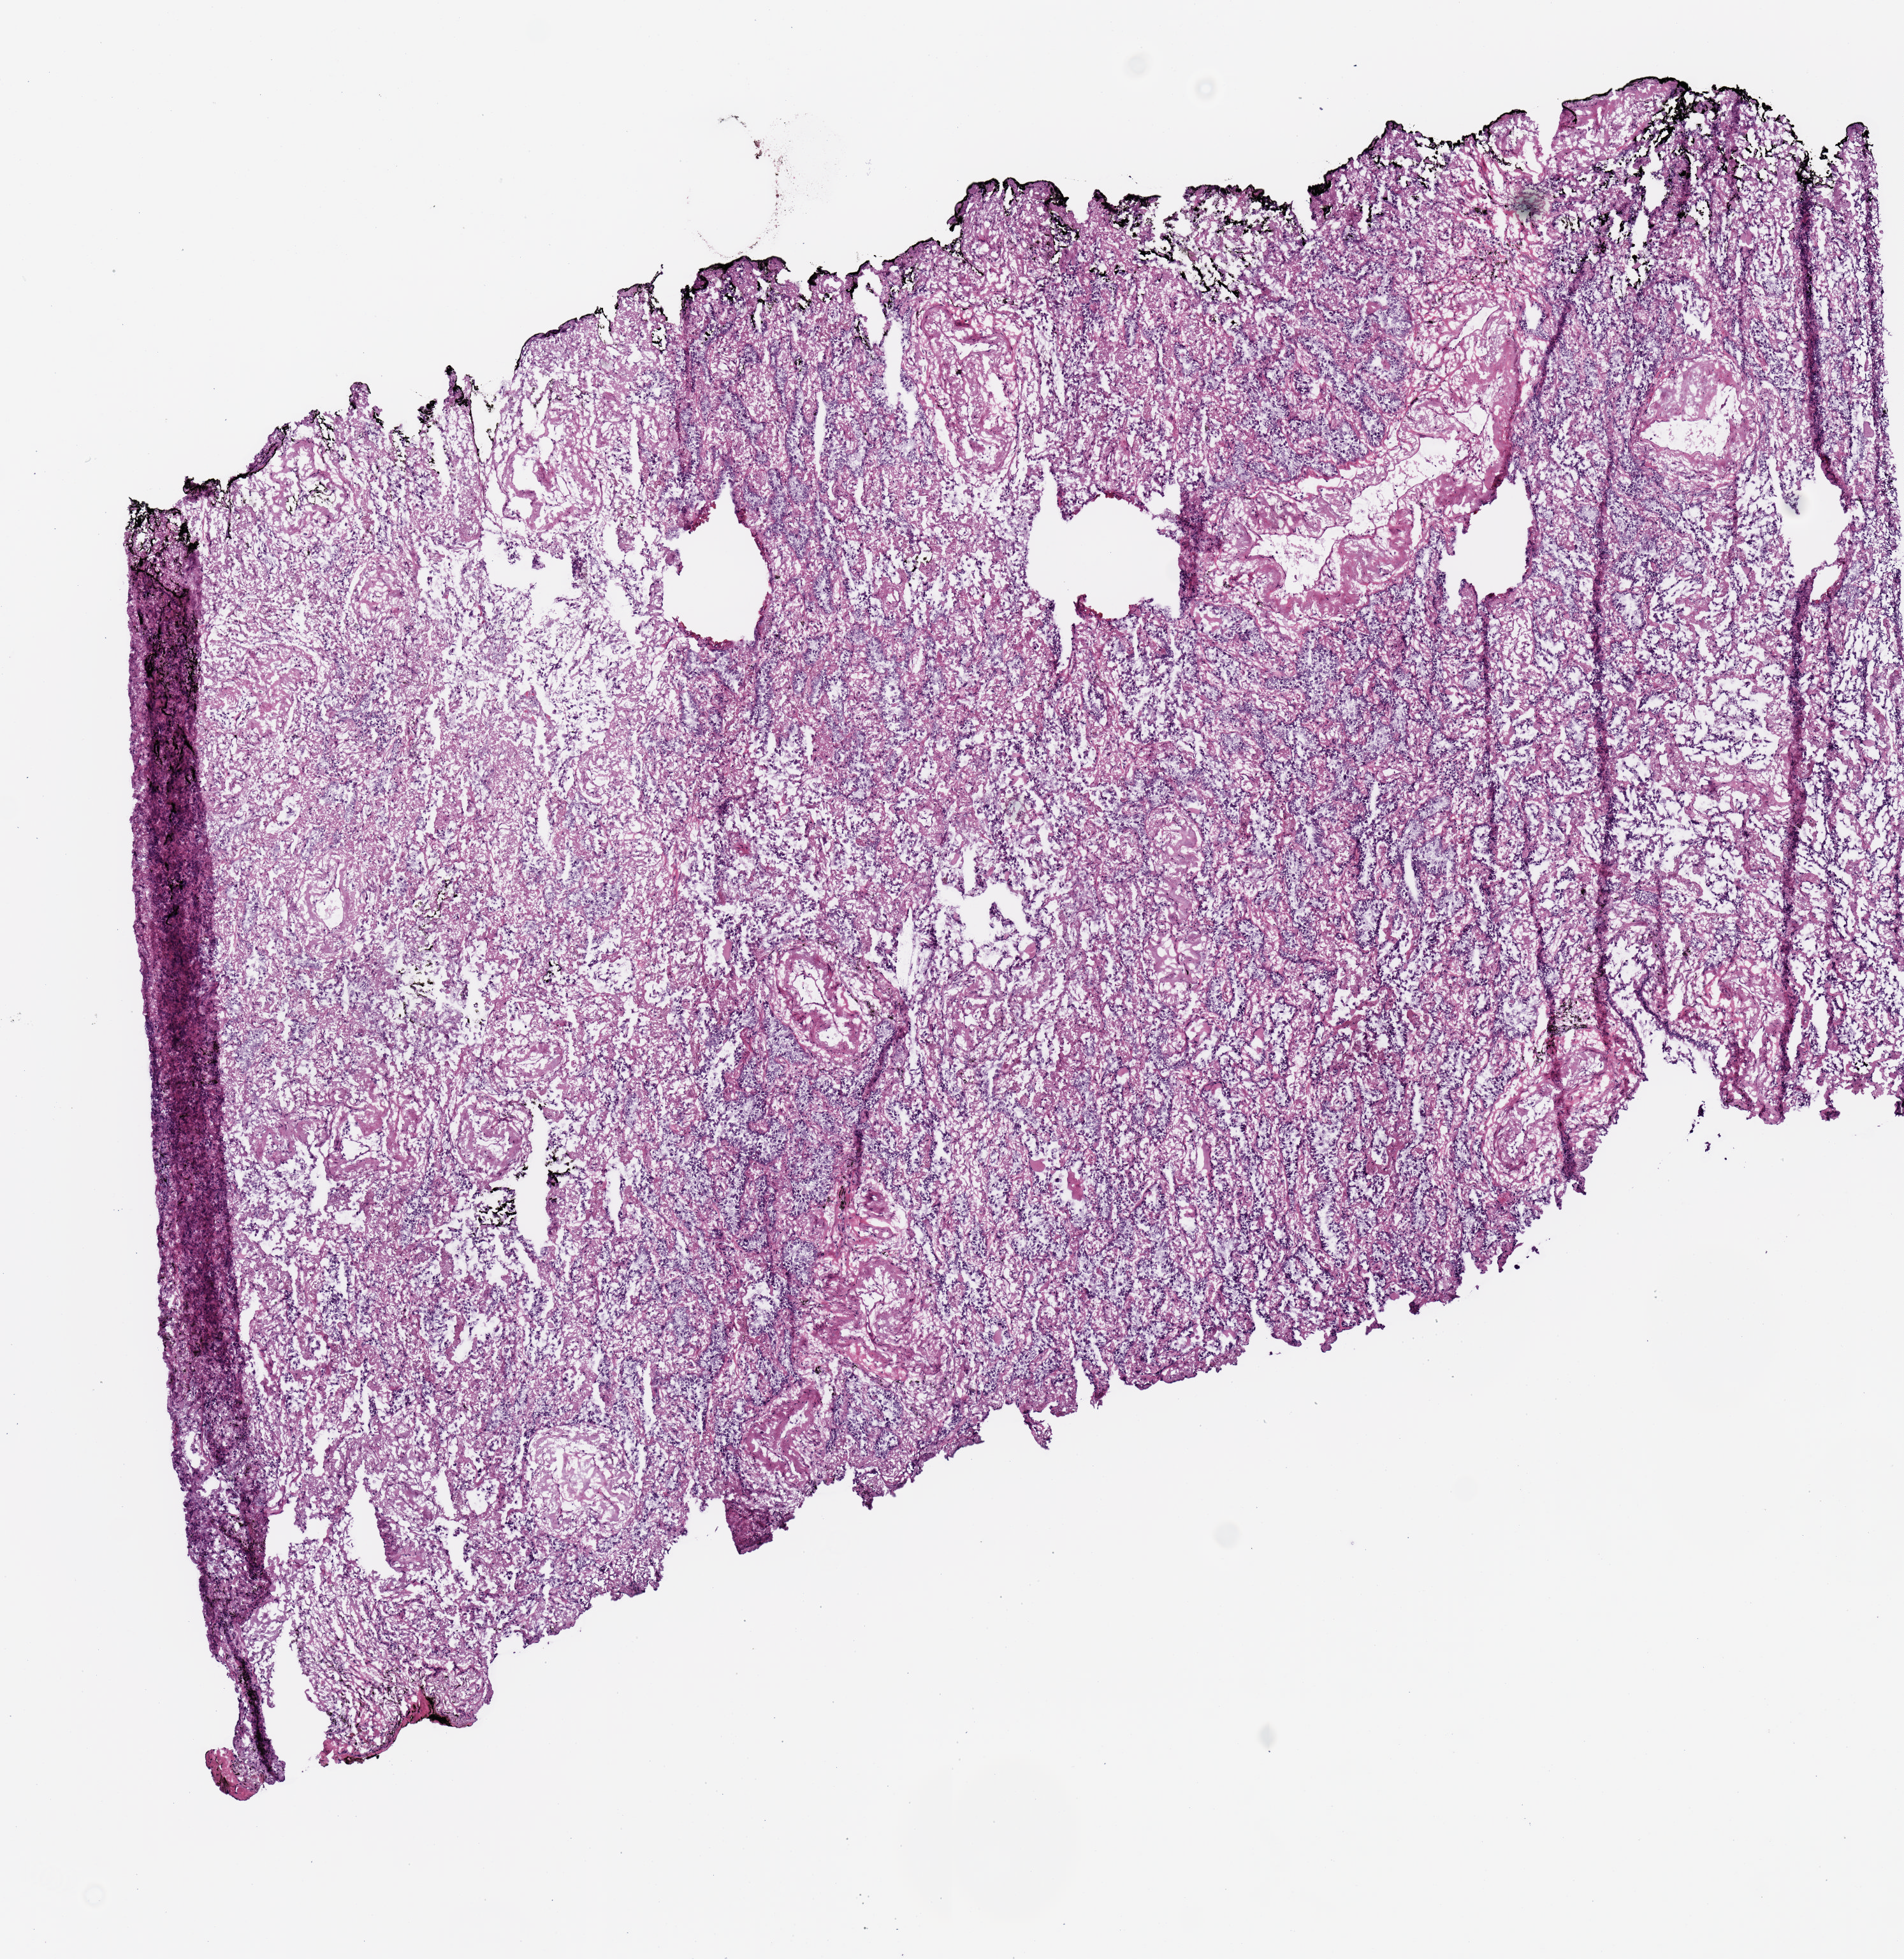
H&E-stained whole-slide image — whole scanned area (about 5.9 x 6.1 mm) shown as a low-resolution overview; frozen section; lung, primary tumour sample. Male patient; age at initial diagnosis 73 years. Composition of this section per pathologist review: tumour cells 0%, tumour nuclei 80%, normal cells 0%, stromal cells 0%, necrosis 0%.
• pathologic diagnosis: Acinar cell carcinoma (lower lobe, lung)
• AJCC pathologic stage: IB (7th edition)
• TNM: T2a N0 MX